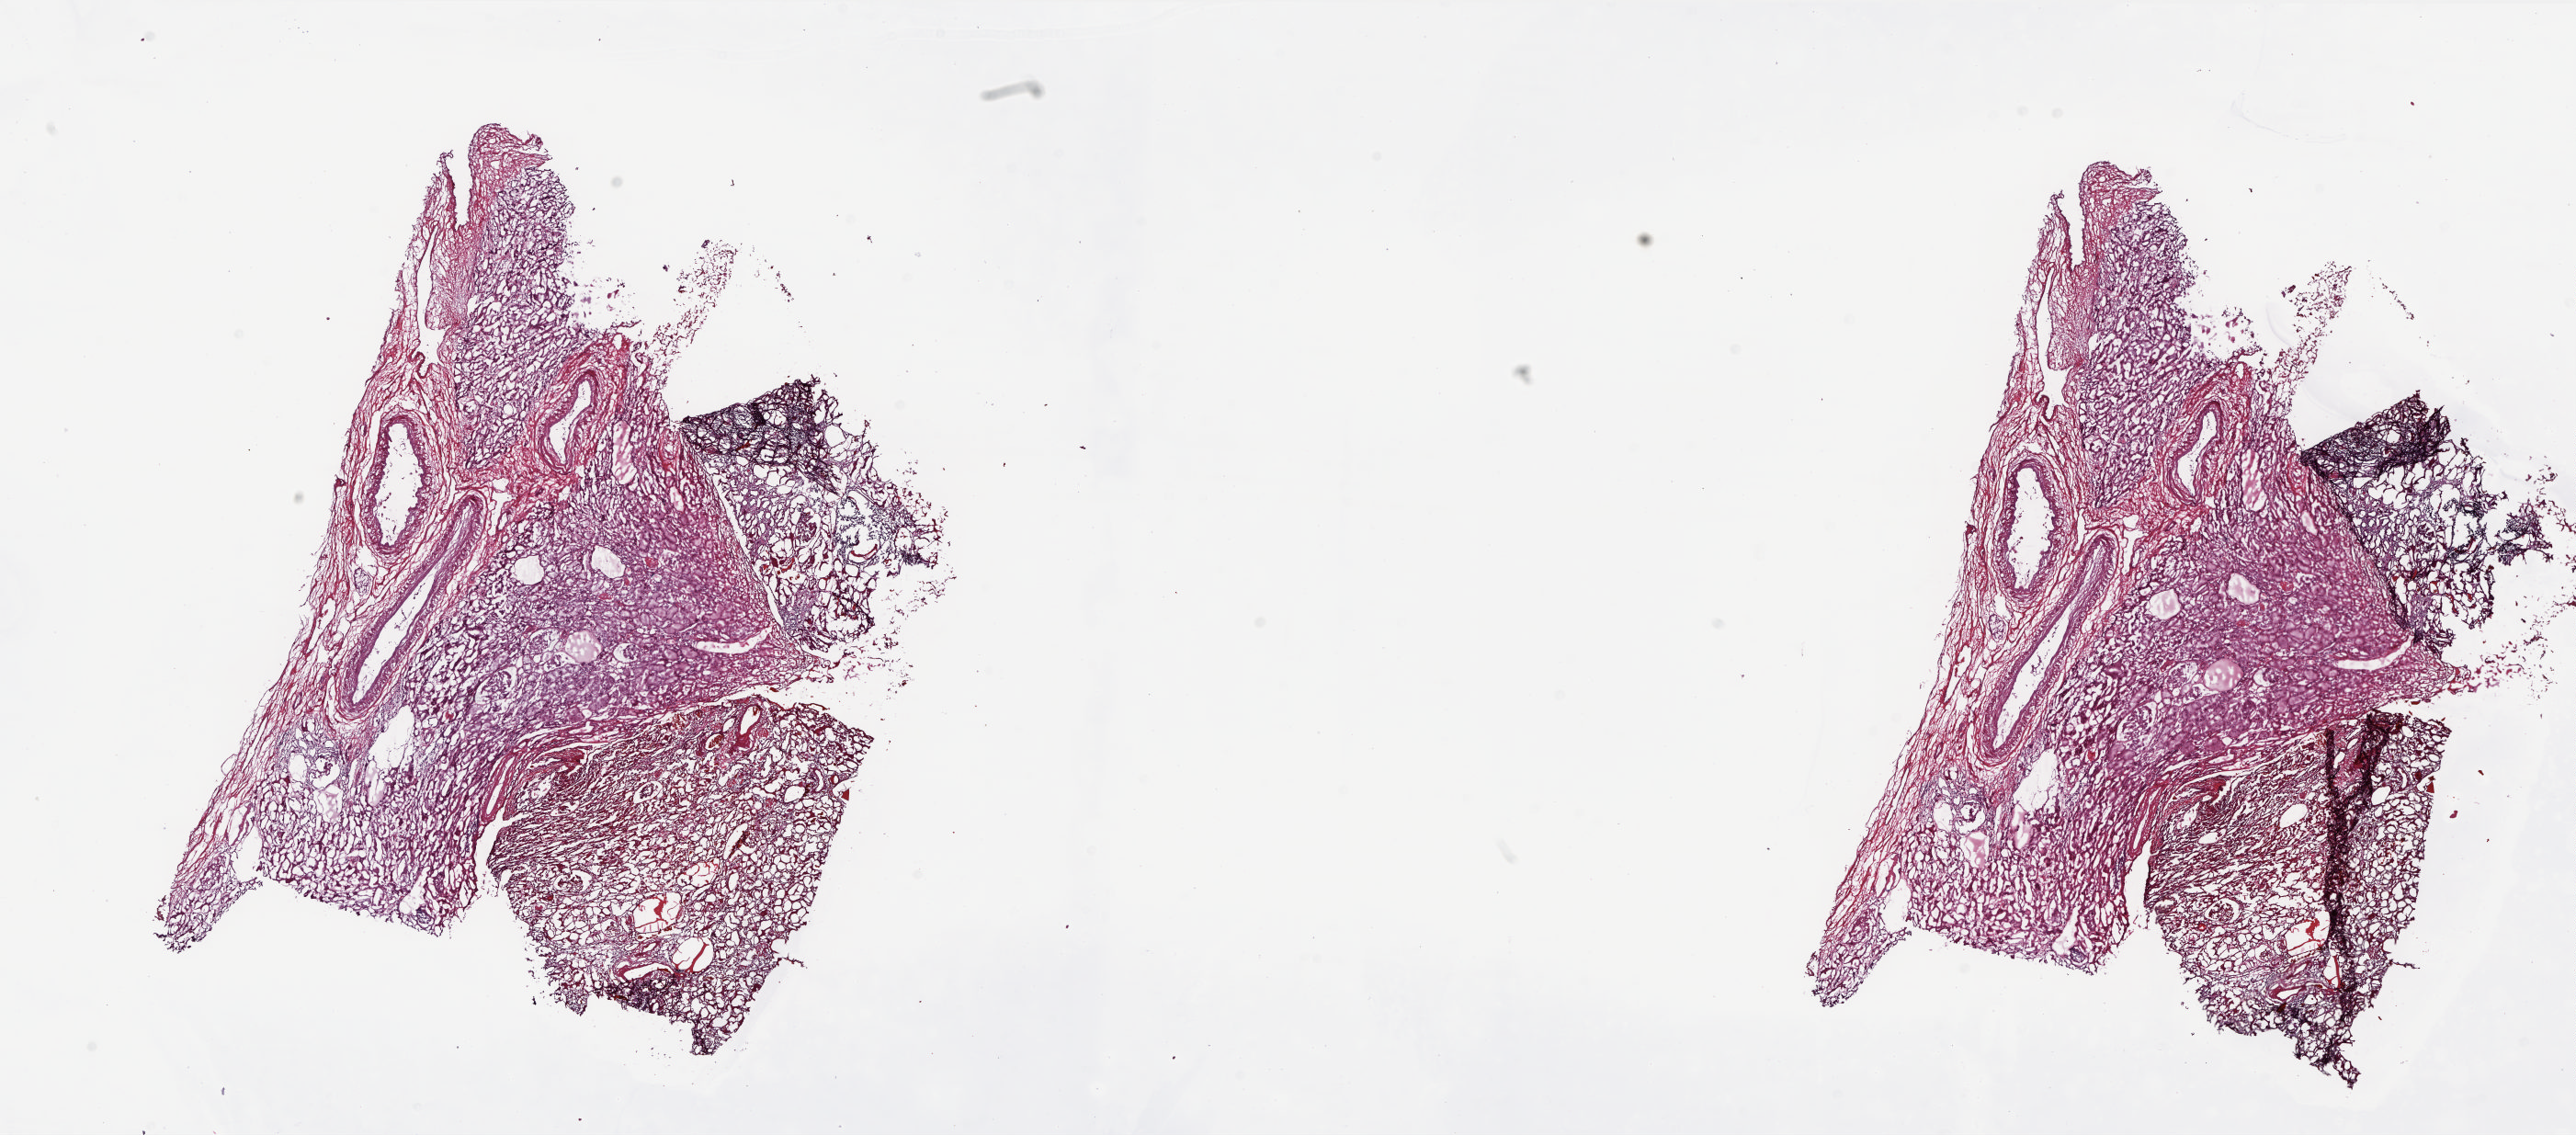
H&E whole-slide image, shown as a low-resolution overview of the whole scanned area (about 22.6 x 10.0 mm, acquisition: 20x scan). Frozen section from the top of the tissue portion. Solid tissue normal (non-tumour tissue) sample from the kidney. Male patient; age at initial diagnosis 67 years.
This section: solid tissue normal sample (biorepository sample class). Patient diagnosis: Papillary adenocarcinoma, NOS.